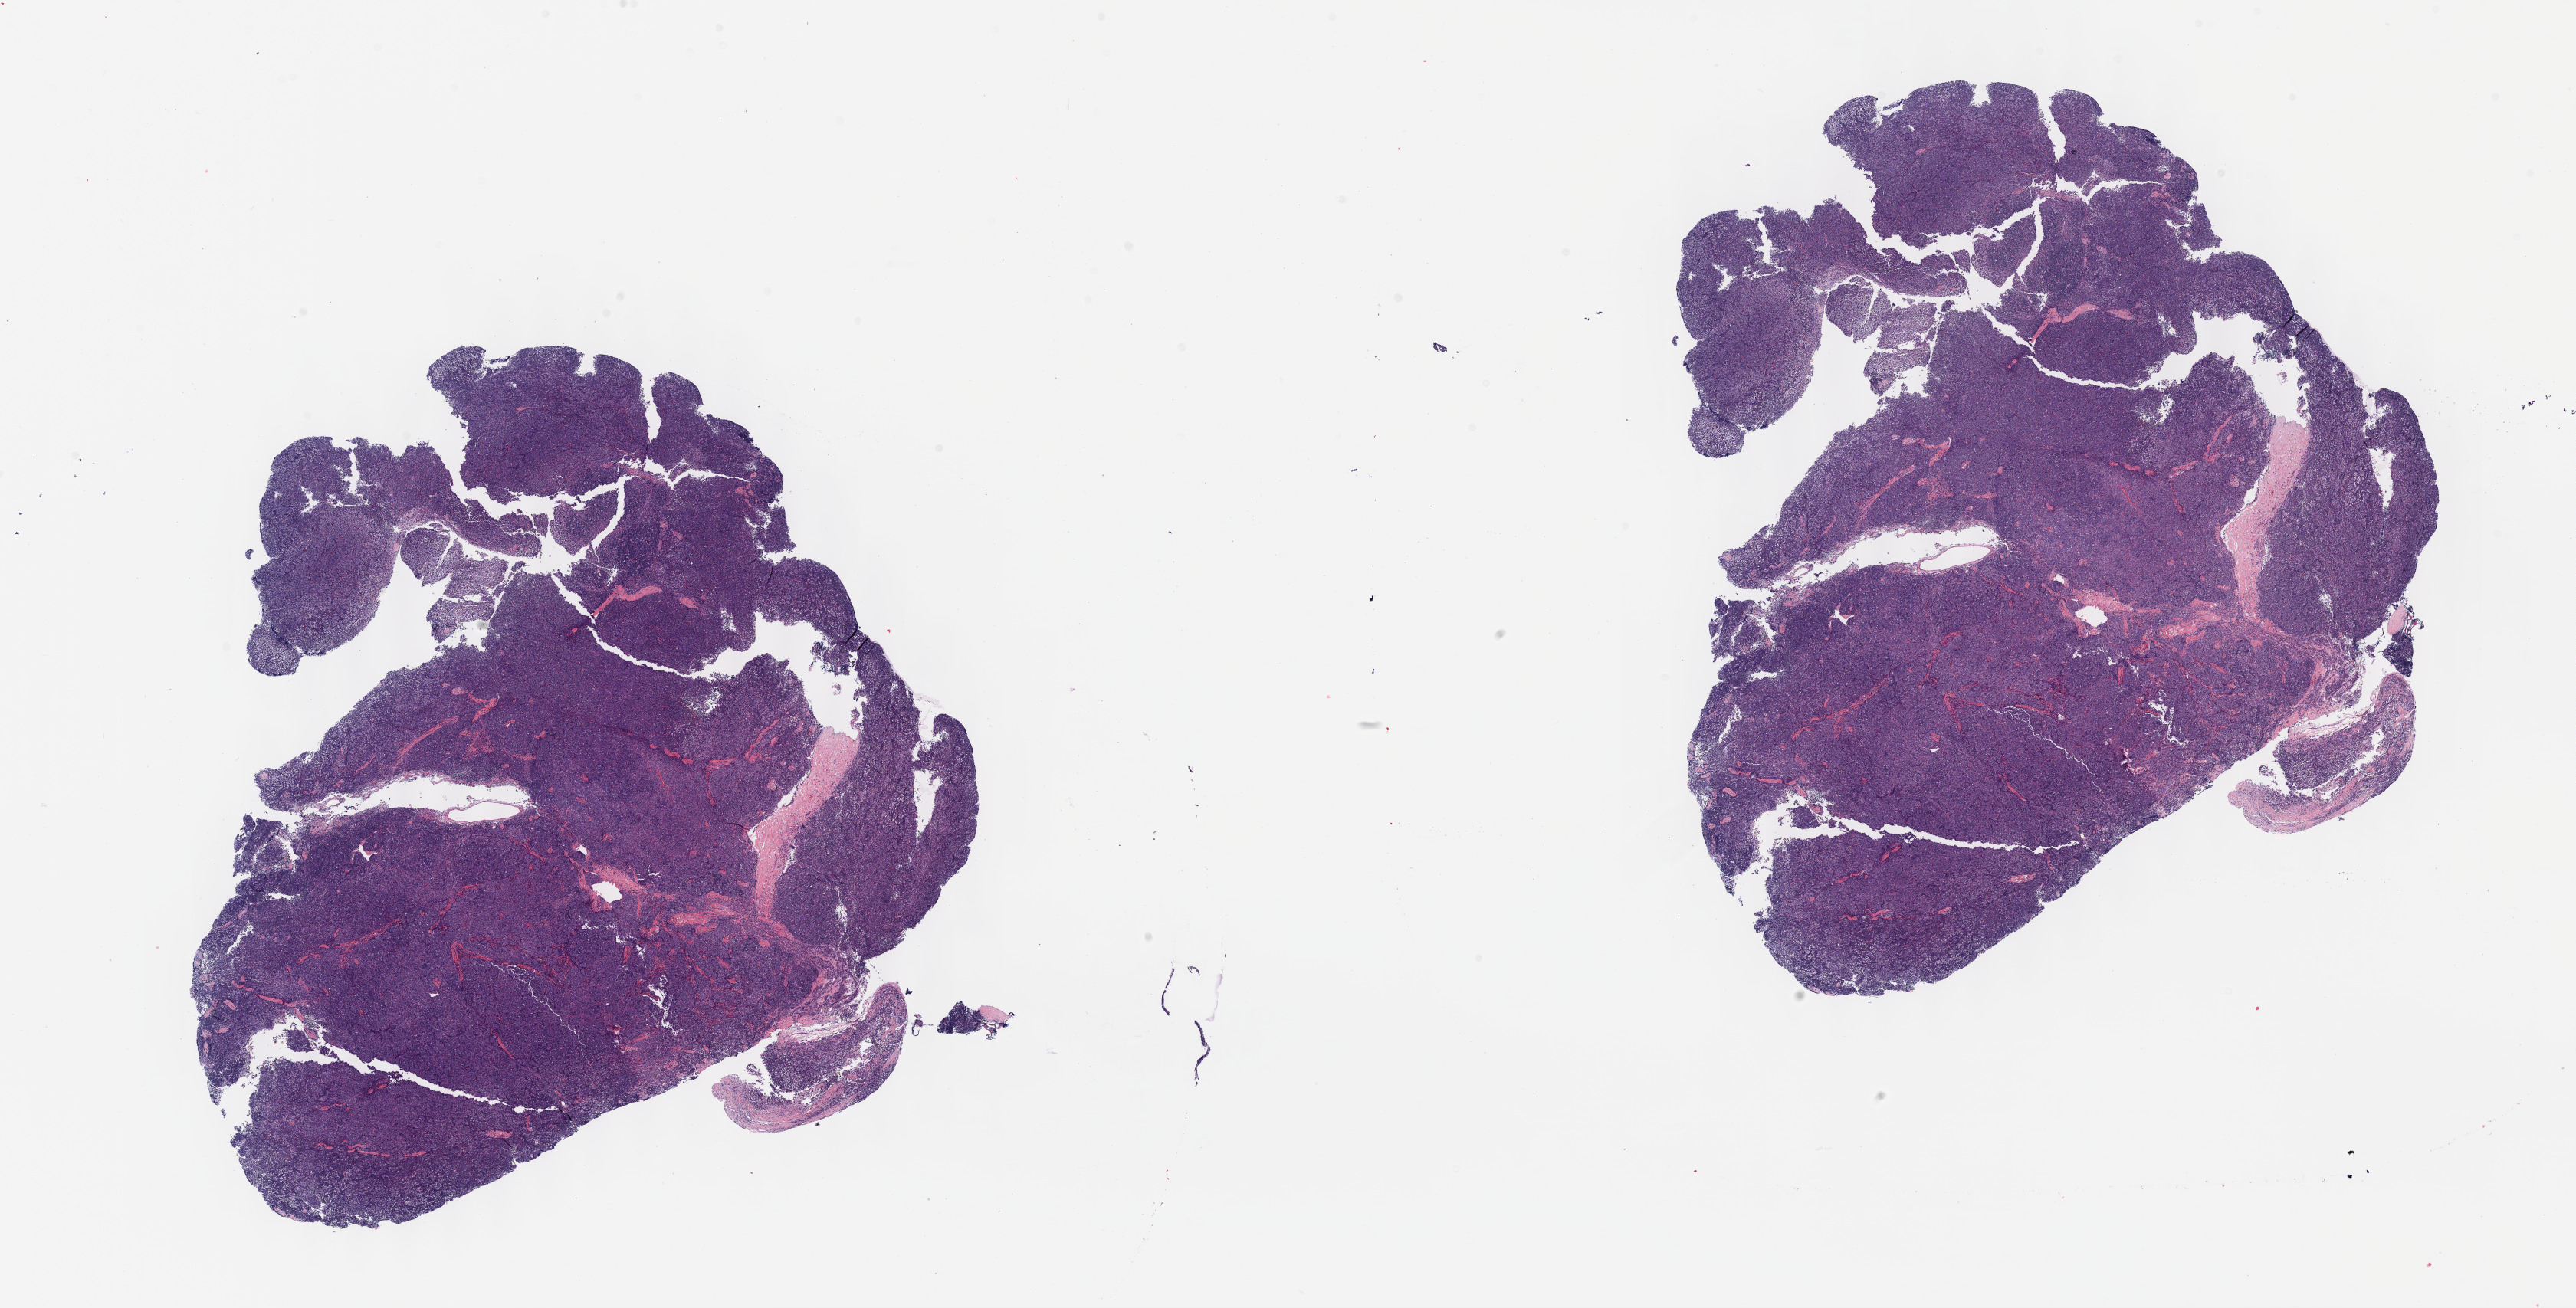
Digitized H&E tissue section (whole slide), low-resolution overview of the scanned area, about 27.2 x 13.8 mm (slide scanned at 40x). Formalin-fixed paraffin-embedded (FFPE) diagnostic section. Sample: primary tumour, thymus. Patient sex: female.
Pathologic diagnosis: Thymoma, type AB, malignant.